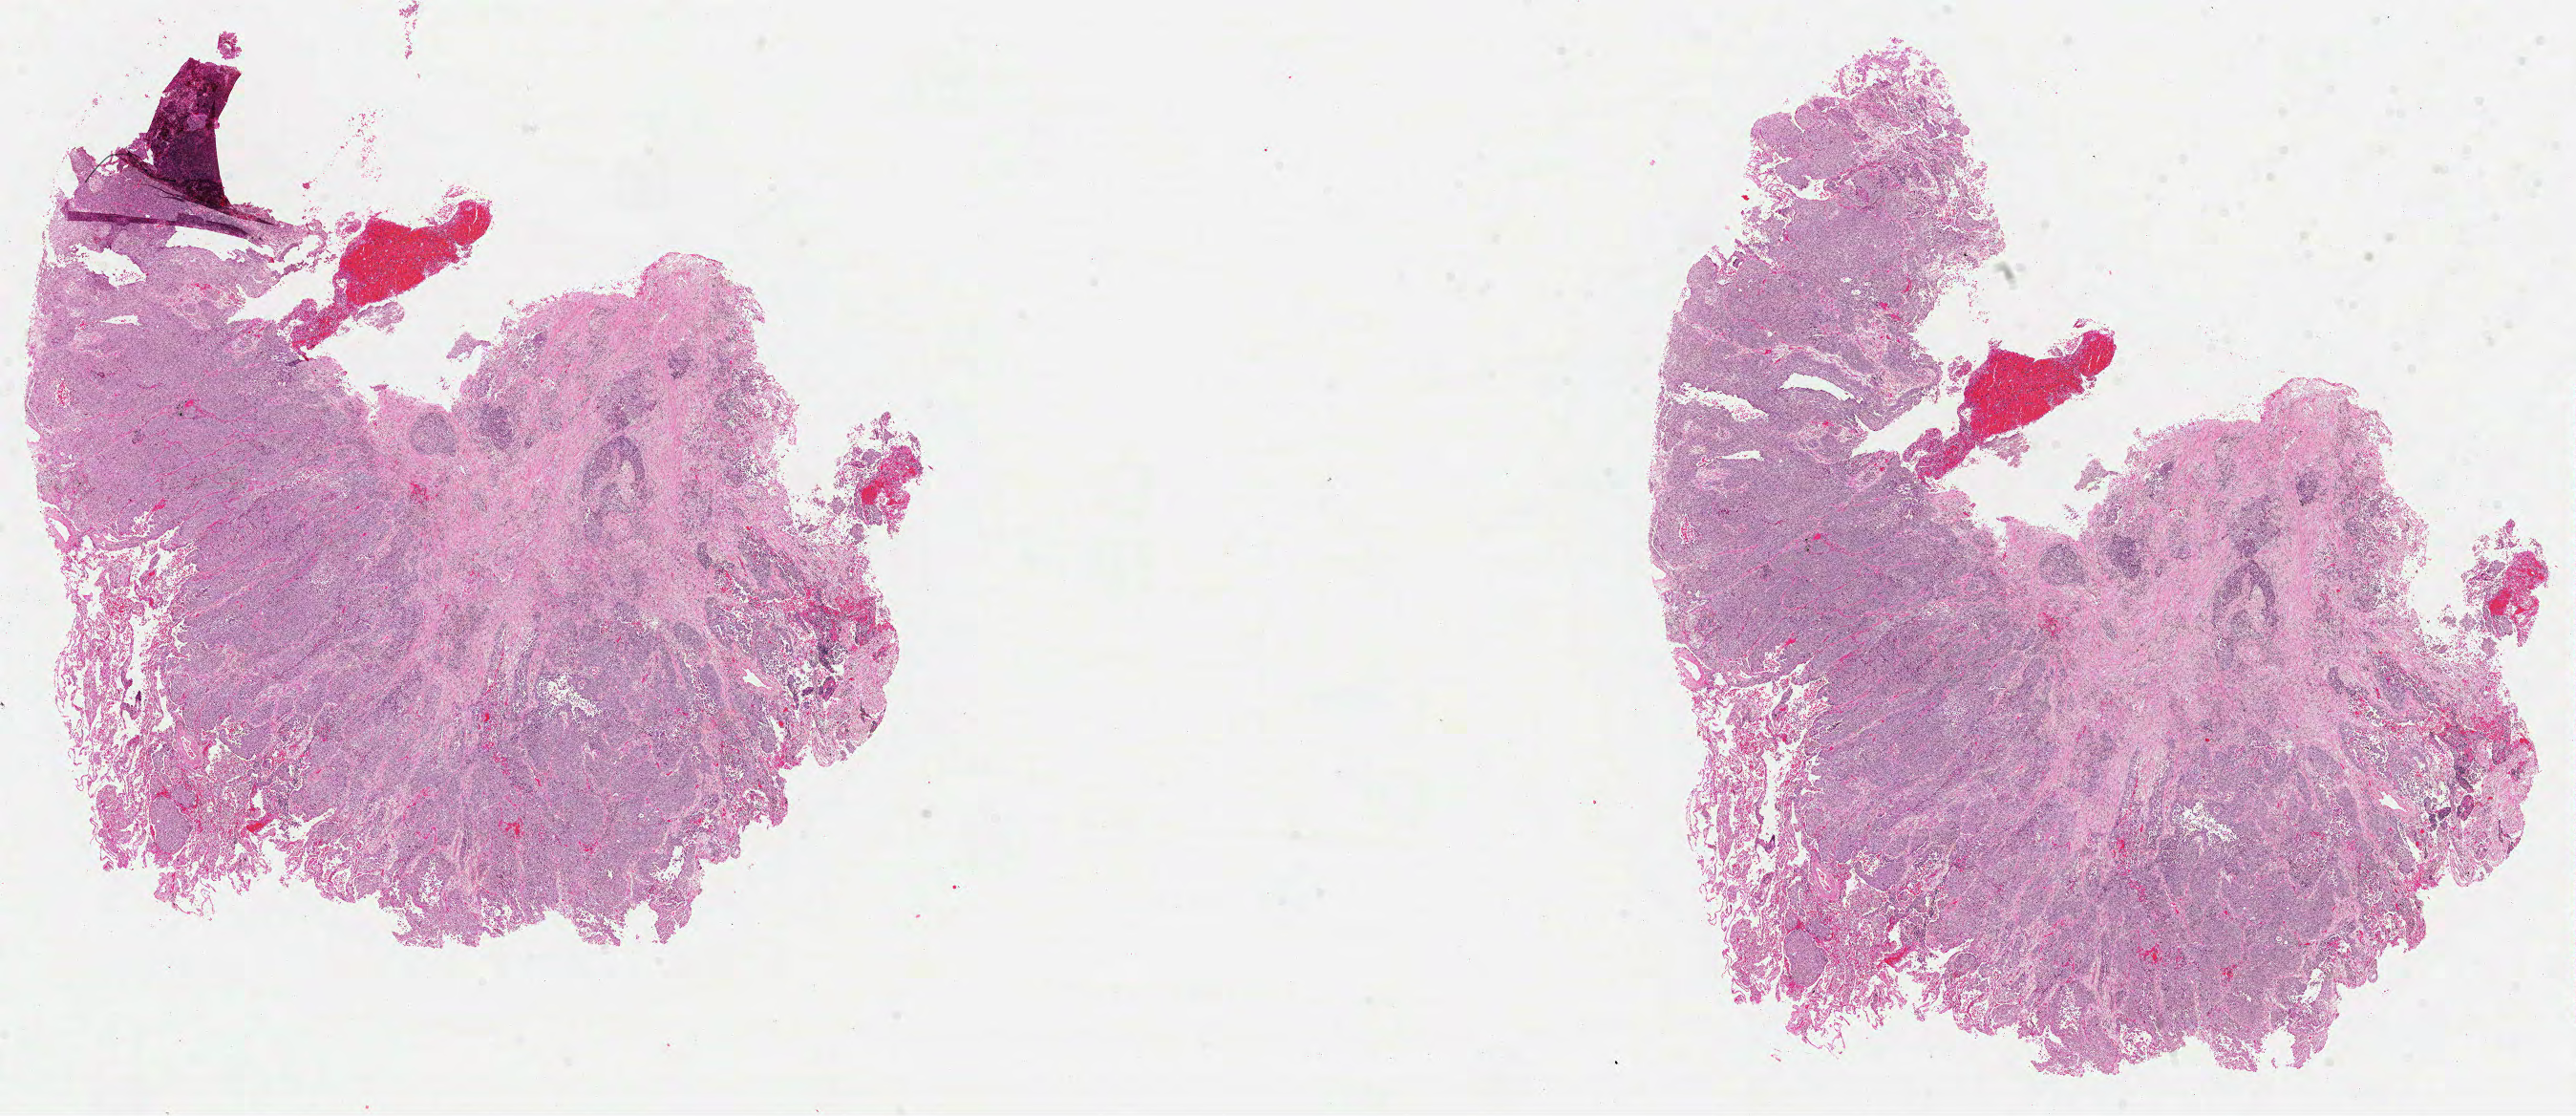
Whole-slide histology image, Hematoxylin and eosin (H&E) stained — low-resolution overview of the scanned area, about 21.8 x 9.4 mm (from a 40x scan). Formalin-fixed paraffin-embedded (FFPE) diagnostic section. Sample: primary tumour, lung. Patient: female, age at initial diagnosis 72 years.
AJCC pathologic stage: I (6th edition). TNM: T1 N0 M0. Histologic diagnosis: Squamous cell carcinoma, NOS (upper lobe, lung).